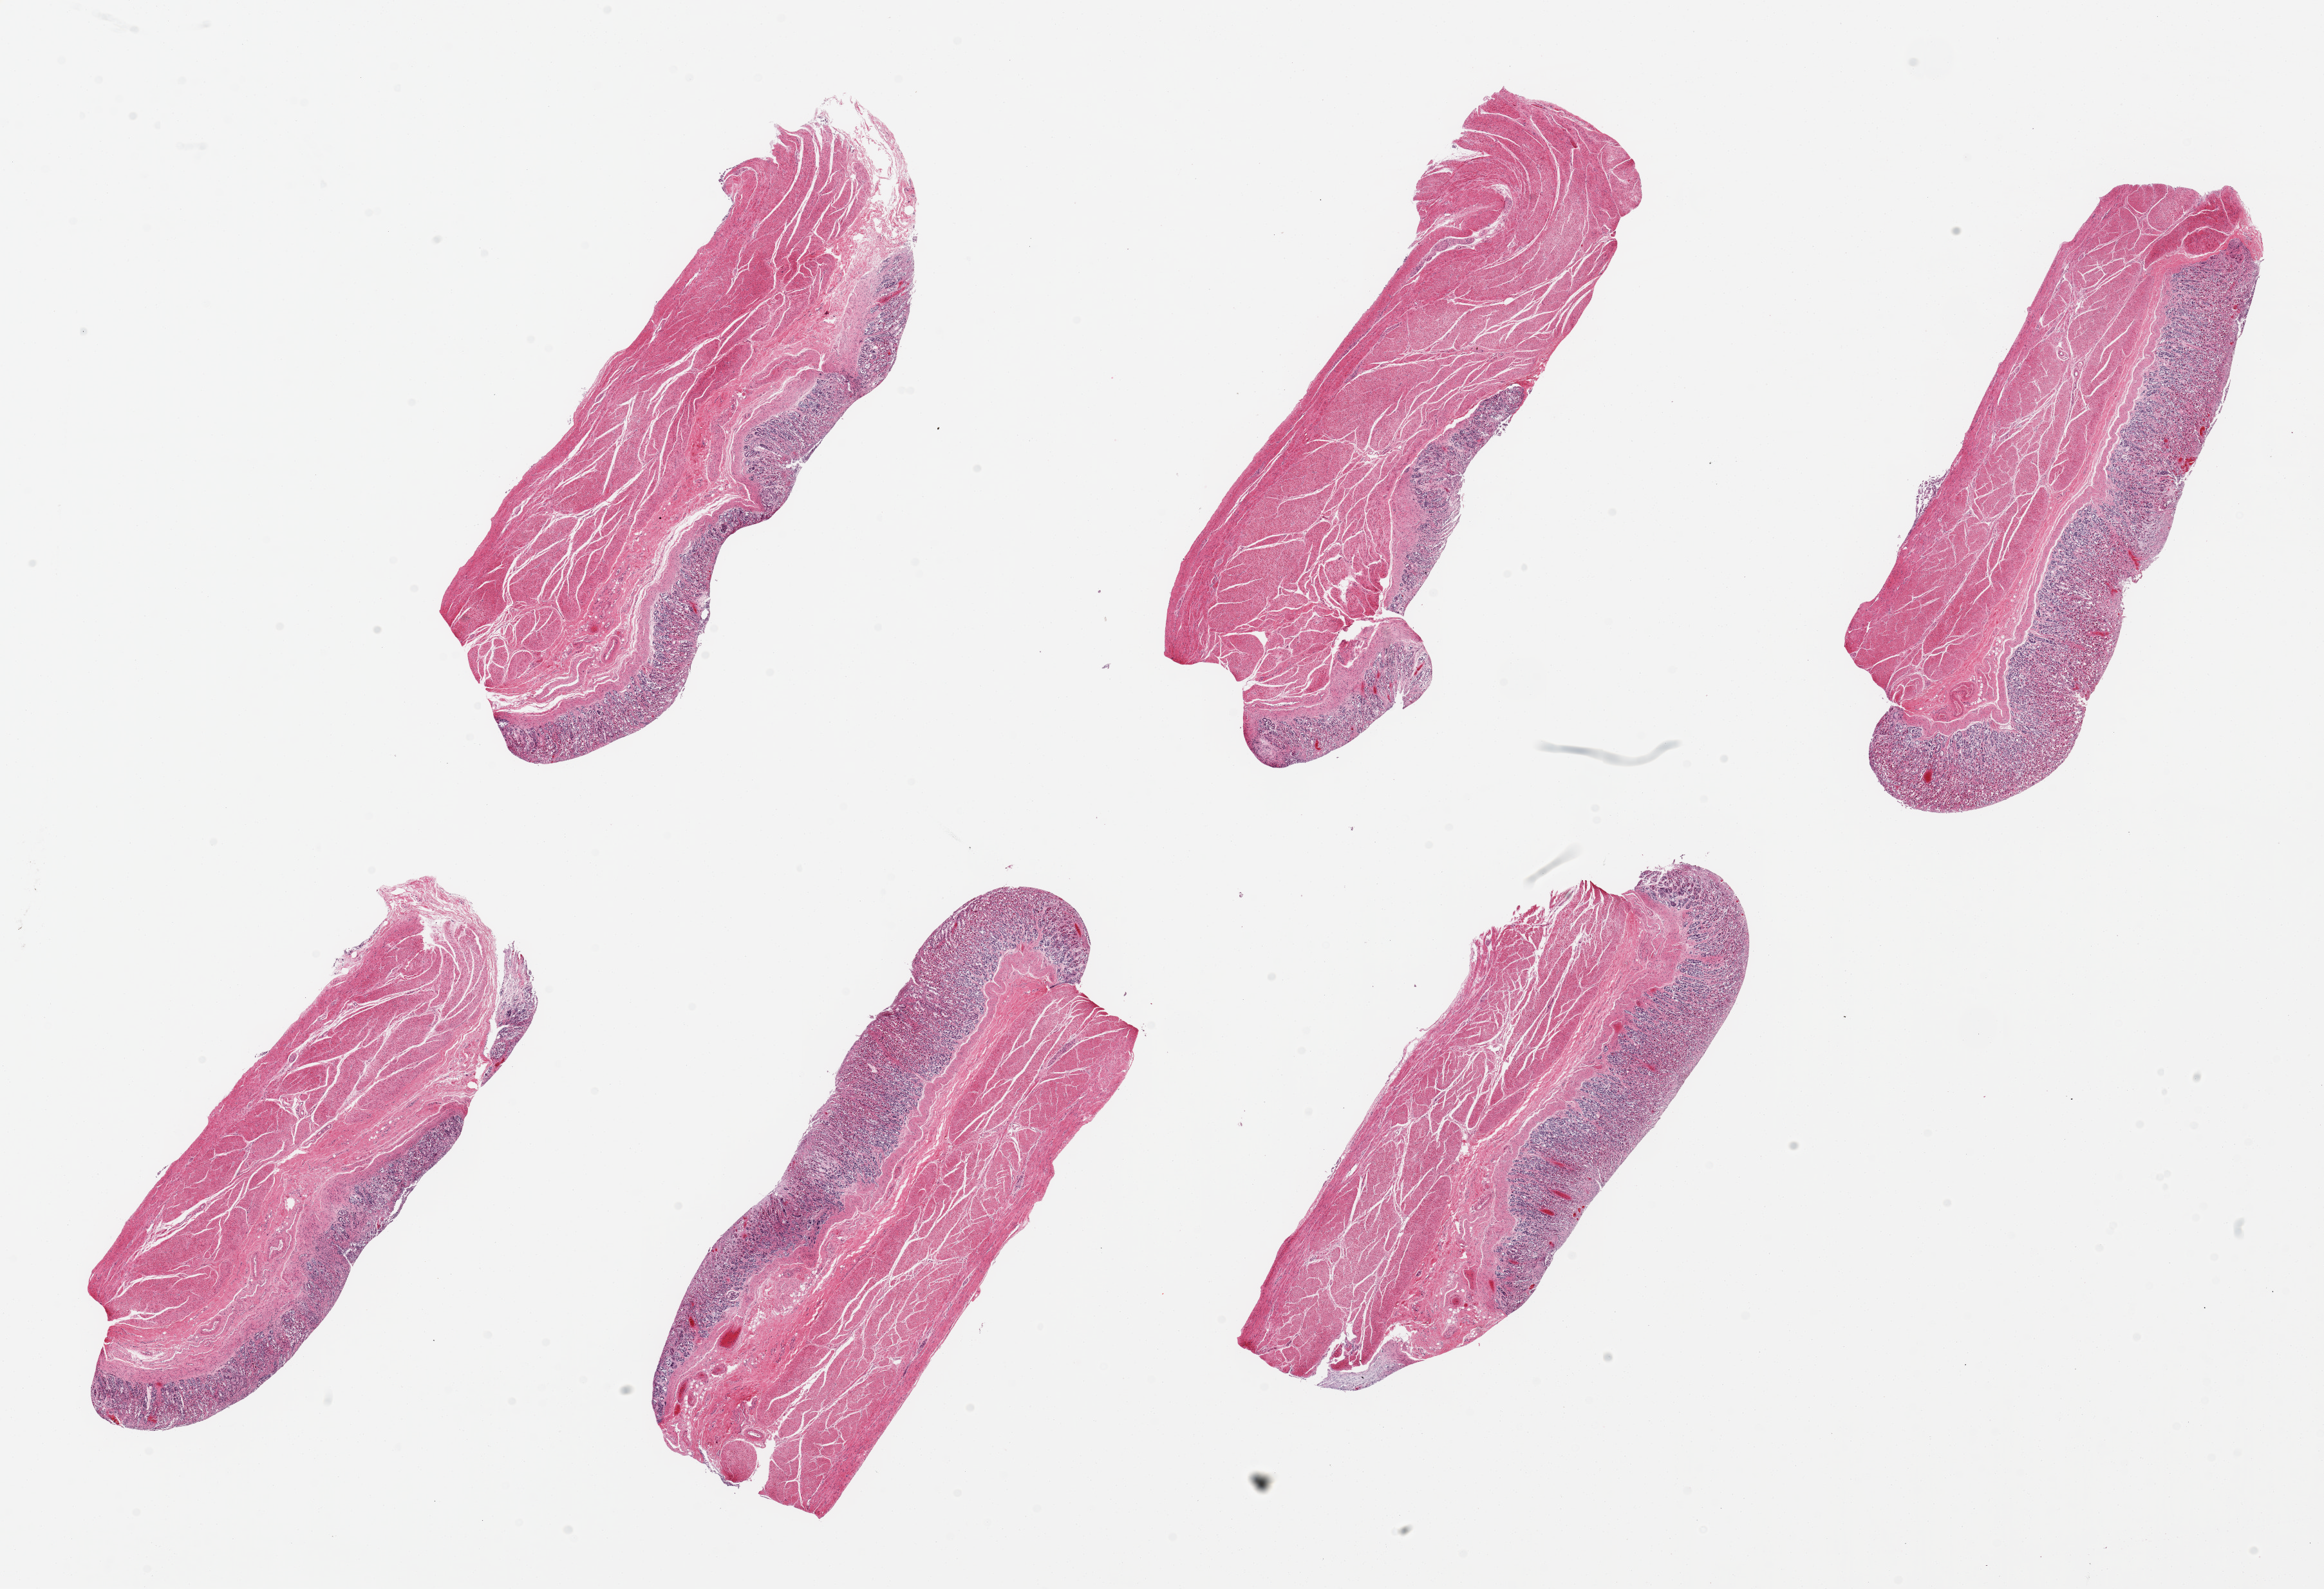
Hematoxylin and eosin (H&E) whole-slide image, brightfield, whole scanned area (about 28.5 x 19.5 mm, slide scanned at 20x) shown as a low-resolution overview. PAXgene-fixed paraffin-embedded (PFPE) section. Sampled site (target tissue): stomach. Donor tissue sample. Donor: male.
Review note (as recorded): 6 pieces up to 9x3.5mm; mucosa ~30-40% thickness but badly autolyzed.